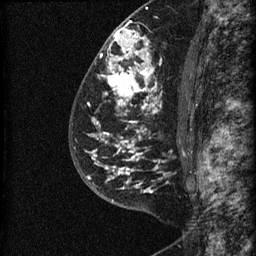
Breast MRI (dynamic contrast-enhanced), one sagittal slice. Dynamic contrast-enhanced series, image 2 of 3 at this slice position (ordered by acquisition). 1.5 T. TE 4.2 ms, TR 22.7 ms. 1.5 mm slice thickness. 256 × 256 image matrix. Patient: female, 48 years. From the clinical record (not read from this slice): setting: breast cancer imaged before/during neoadjuvant chemotherapy; receptor status: triple-negative.
Structures marked on this image (semi-automatically segmented with operator editing):
- analysis volume of interest (the breast-tissue region the enhancement analysis was run in; not a lesion): bounding box [x1, y1, x2, y2] px = [81, 23, 186, 202]
- tumour enhancement mask (voxels above the 90 % enhancement threshold inside the analysis volume of interest): [87, 28, 166, 192]